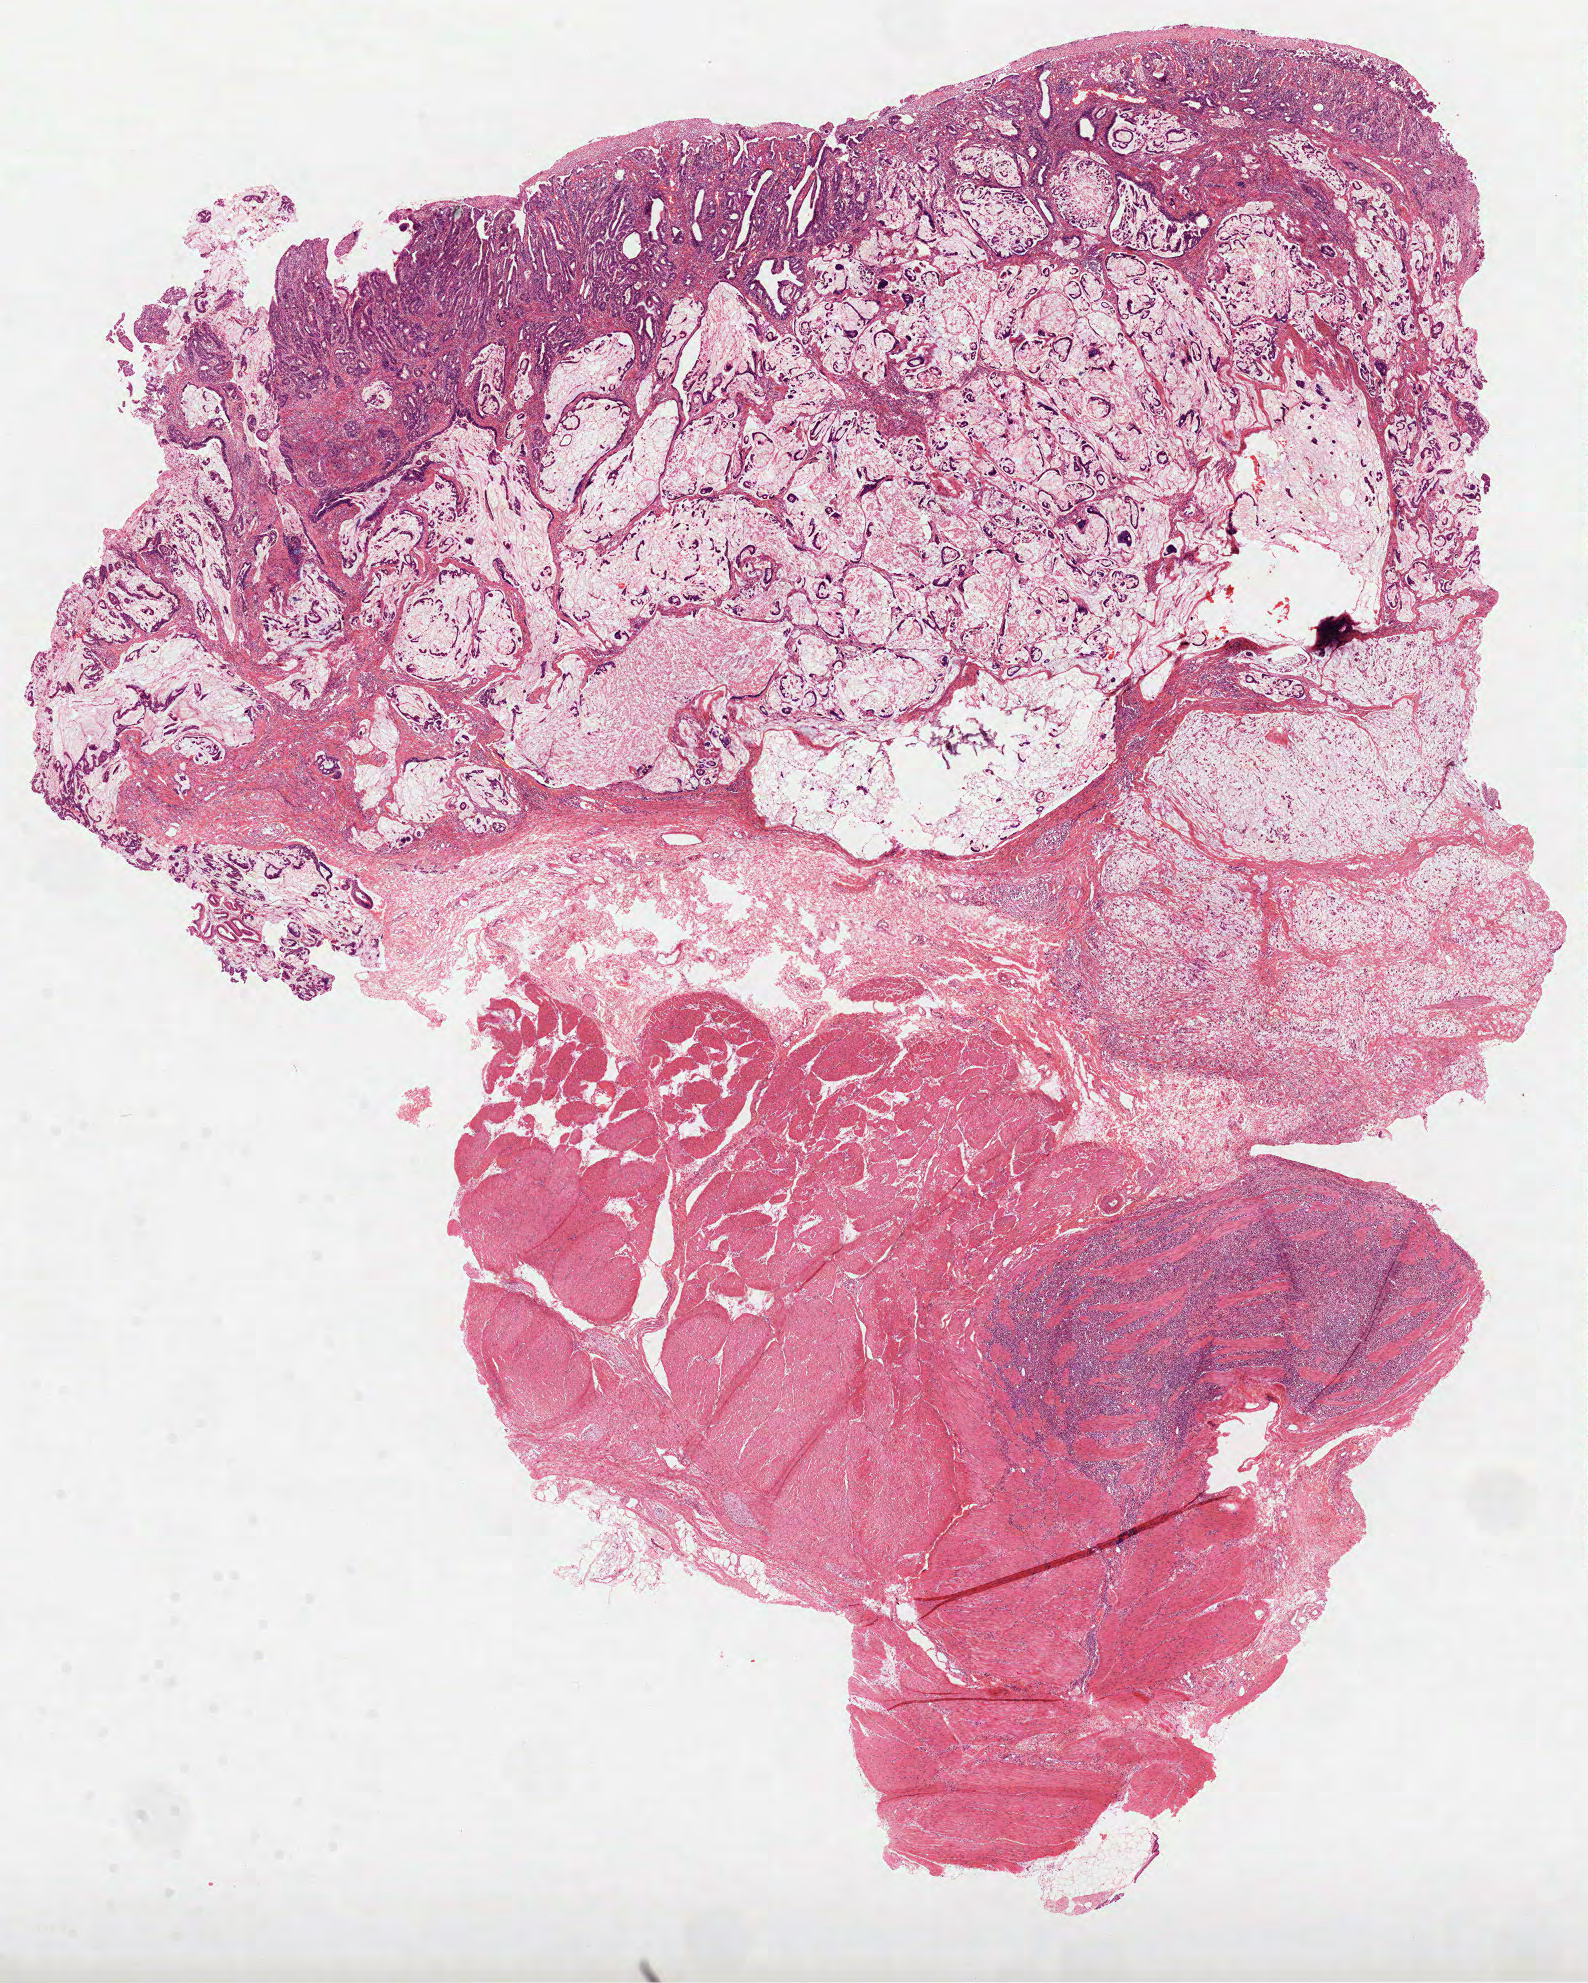
Whole-slide histology image, H&E-stained, a low-resolution overview of the entire scanned area, about 12.8 x 16.0 mm (slide scanned at 40x); formalin-fixed paraffin-embedded (FFPE) diagnostic section; stomach, primary tumour sample. Female patient; age at initial diagnosis 63 years. Histologic grade: G2 (moderately differentiated).
* histologic diagnosis: Adenocarcinoma, NOS
* AJCC pathologic stage: IB